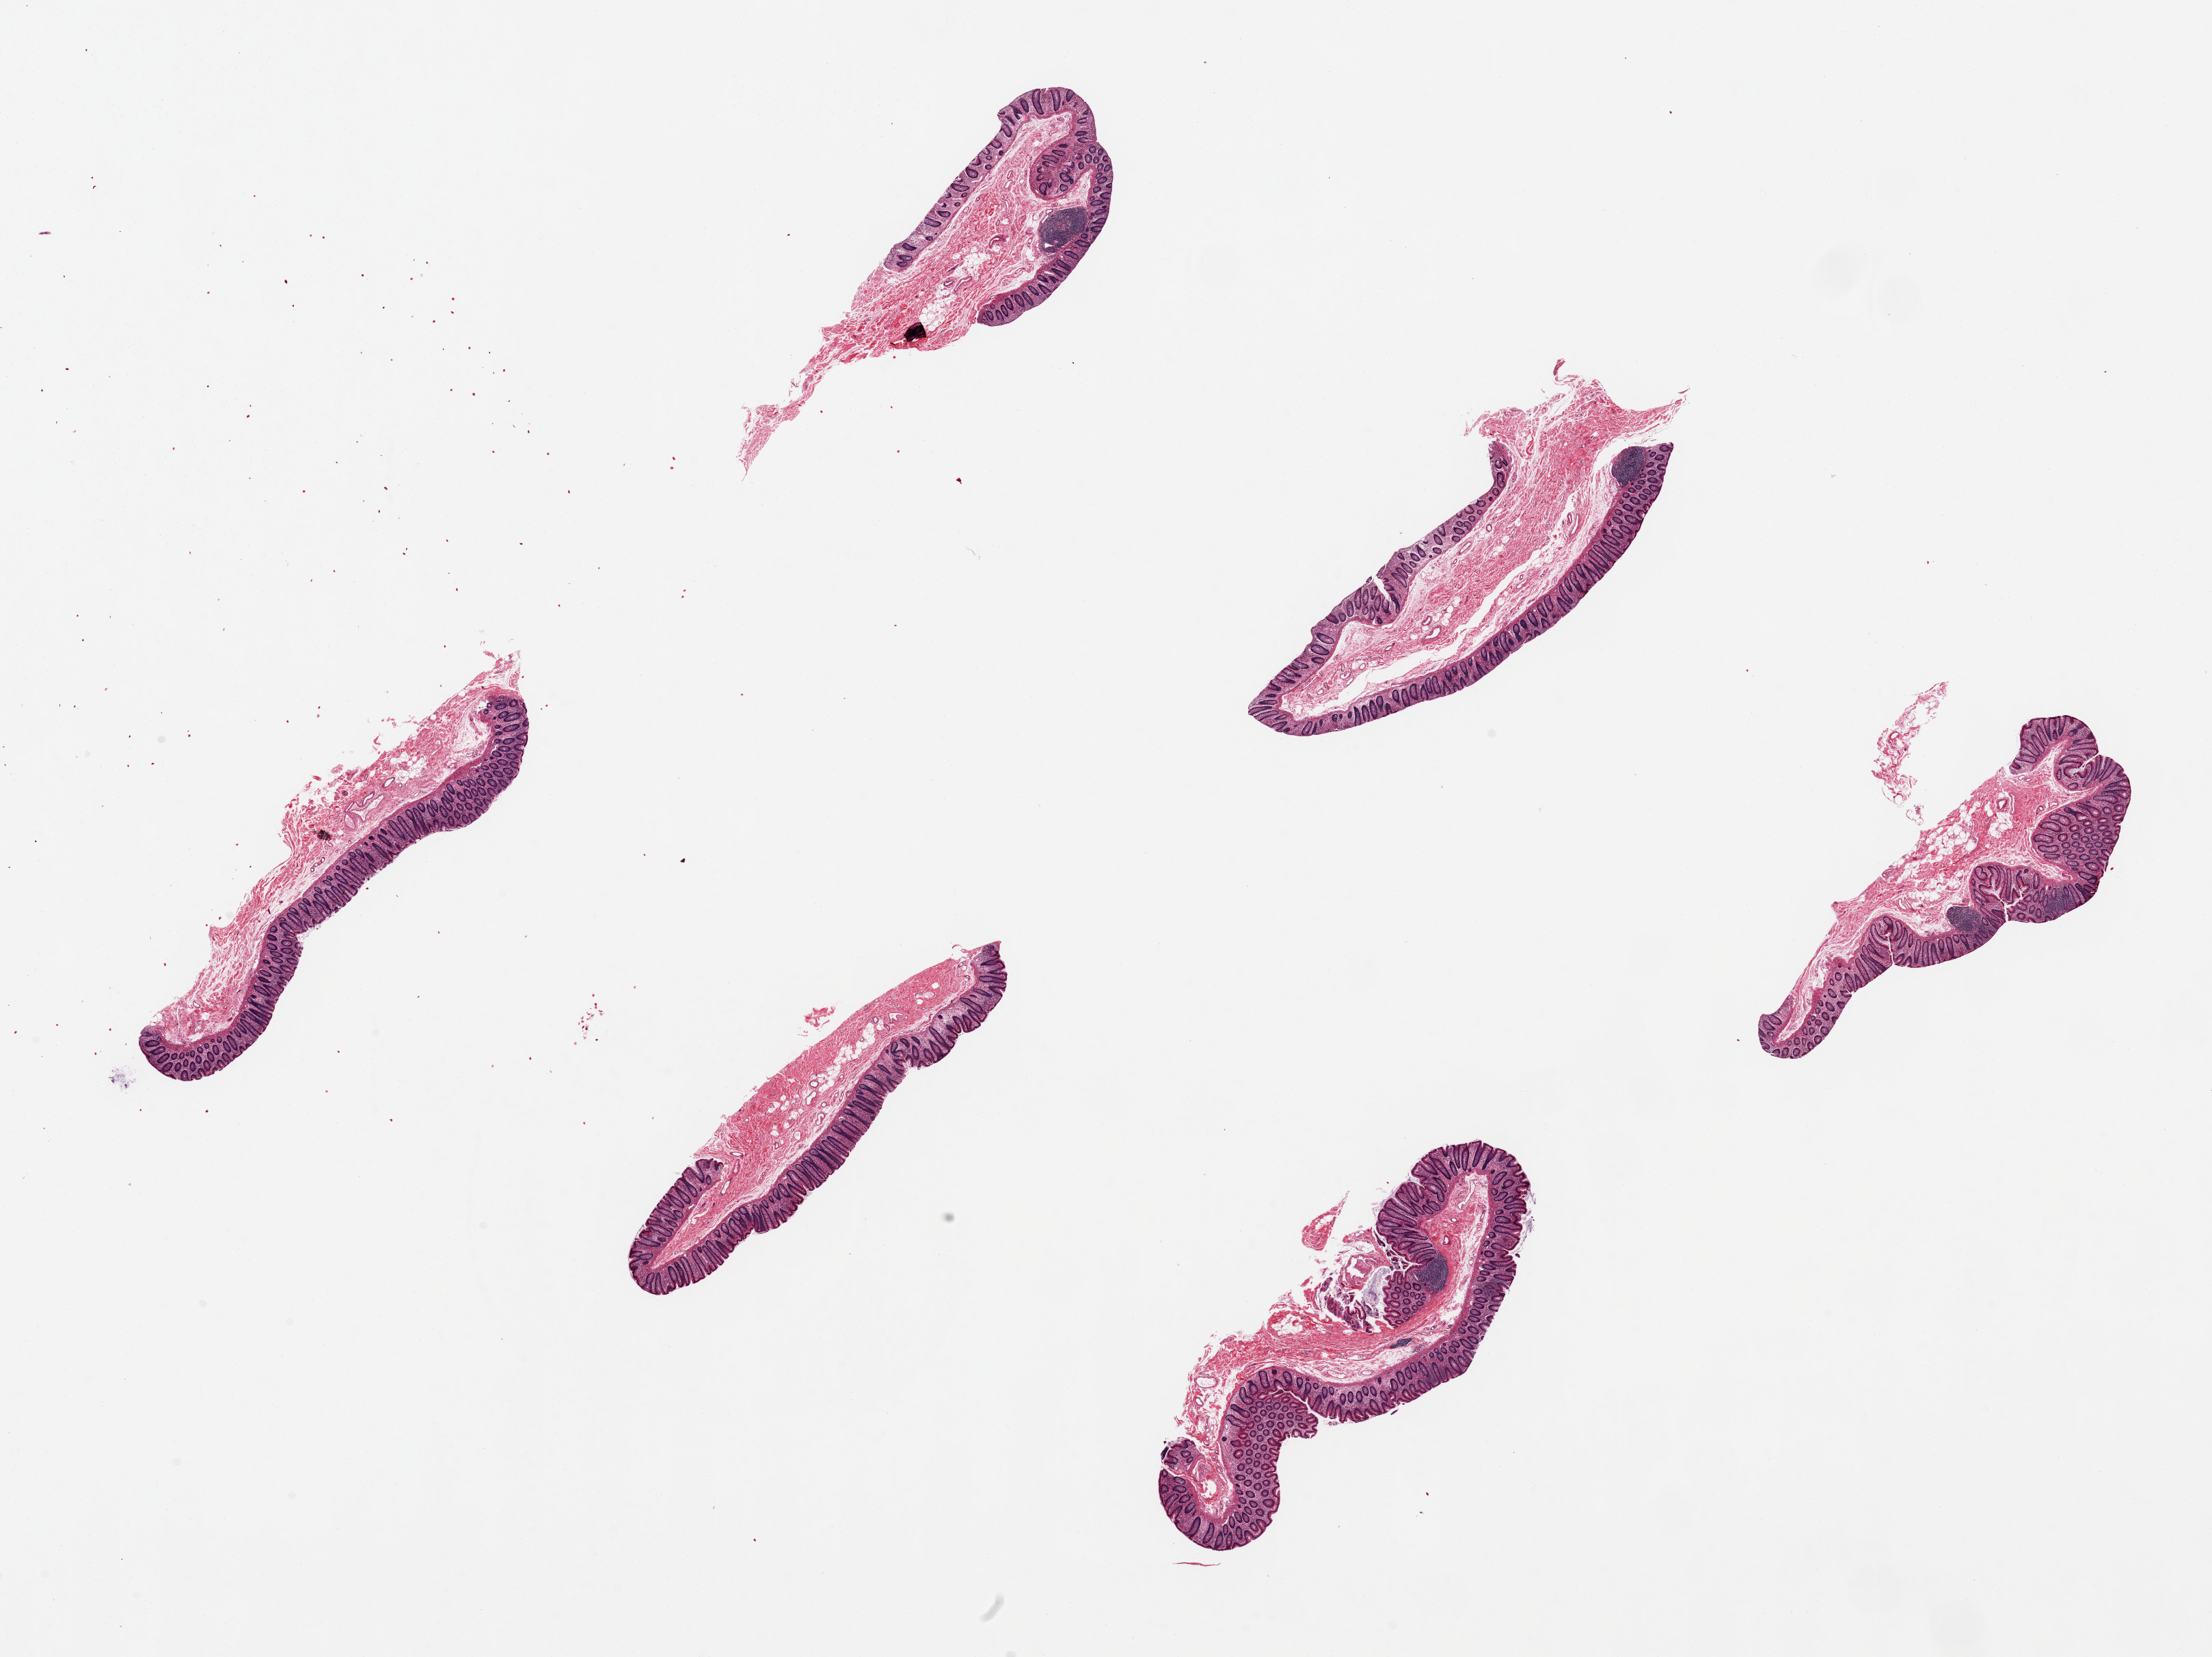
H&E whole-slide image, brightfield, whole scanned area (about 25.6 x 19.2 mm) shown as a low-resolution overview, PAXgene-fixed, paraffin-embedded tissue, sampled site (target tissue): transverse colon, tissue donor sample. Donor sex: male.
* reviewer comment on this tissue sample: 6 pieces, ~6x1.2mm. Mucosa moderately well preserved, ~30% of thickness